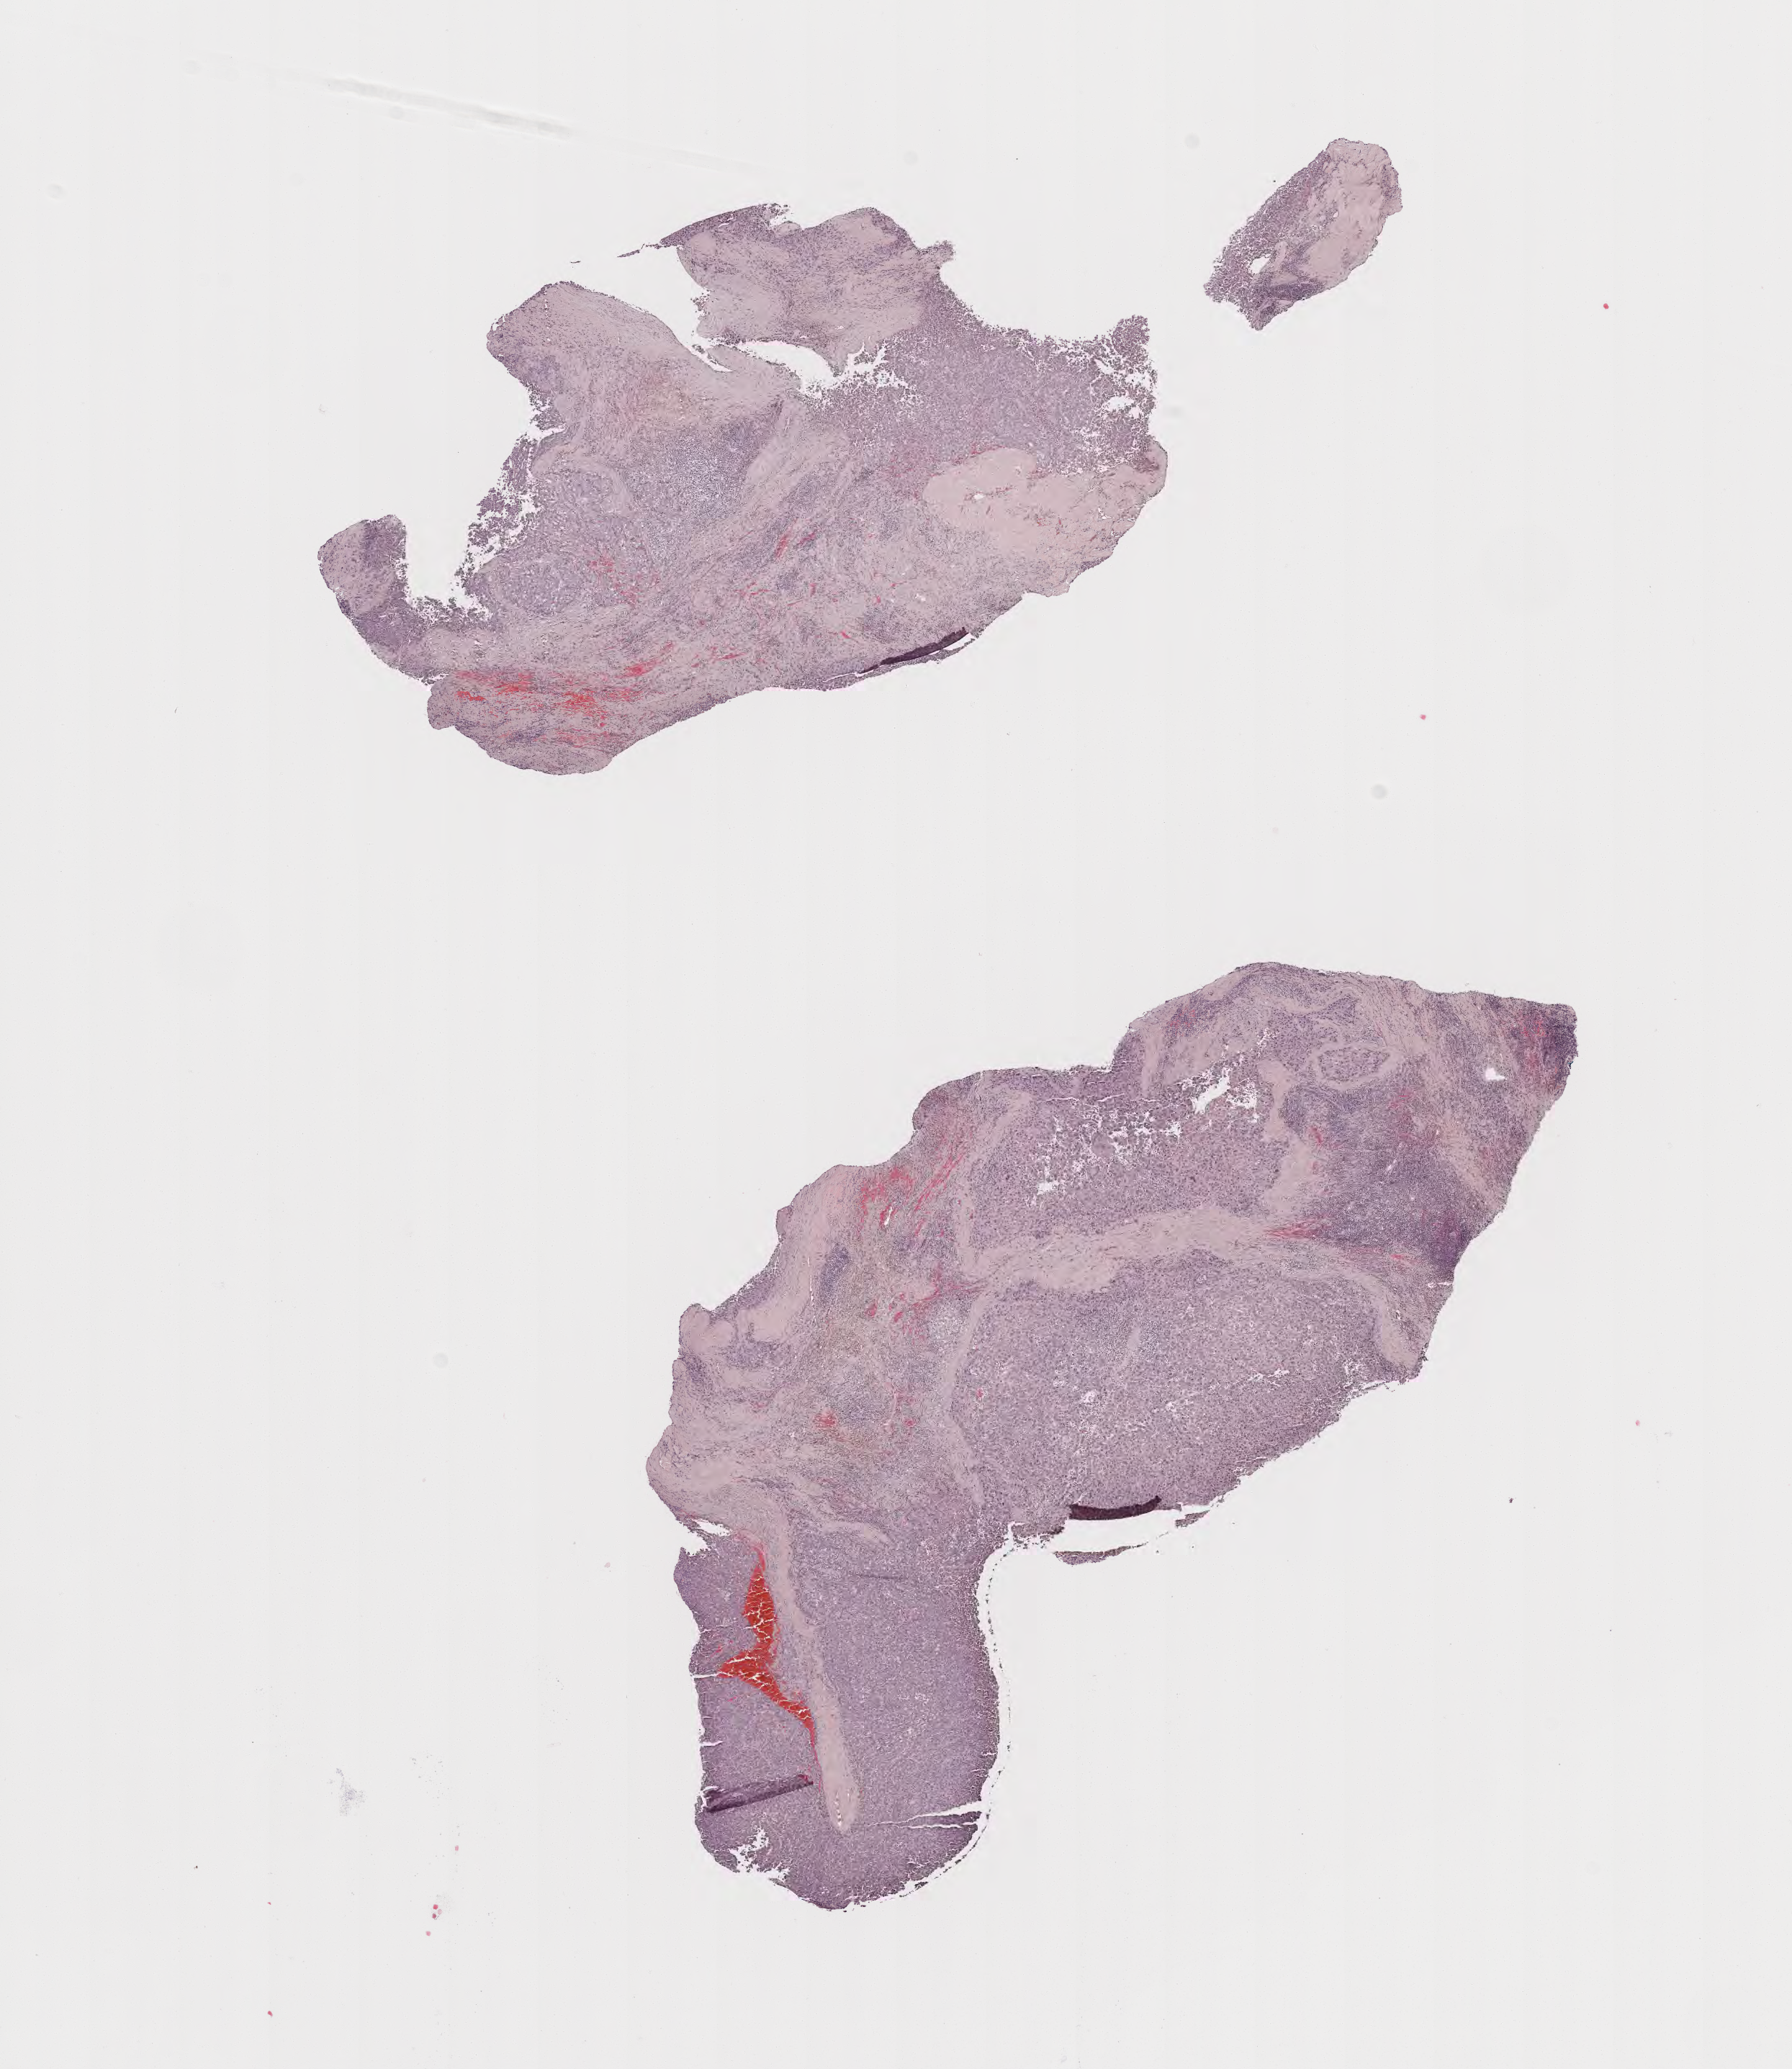
Digitized Hematoxylin and eosin (H&E) stained tissue section (whole slide), low-resolution overview of the scanned area, about 10.1 x 11.6 mm (acquisition: 40x scan); formalin-fixed paraffin-embedded (FFPE) diagnostic section; primary tumour sample from the liver. Male patient.
Diagnosis: Hepatocellular carcinoma, NOS.